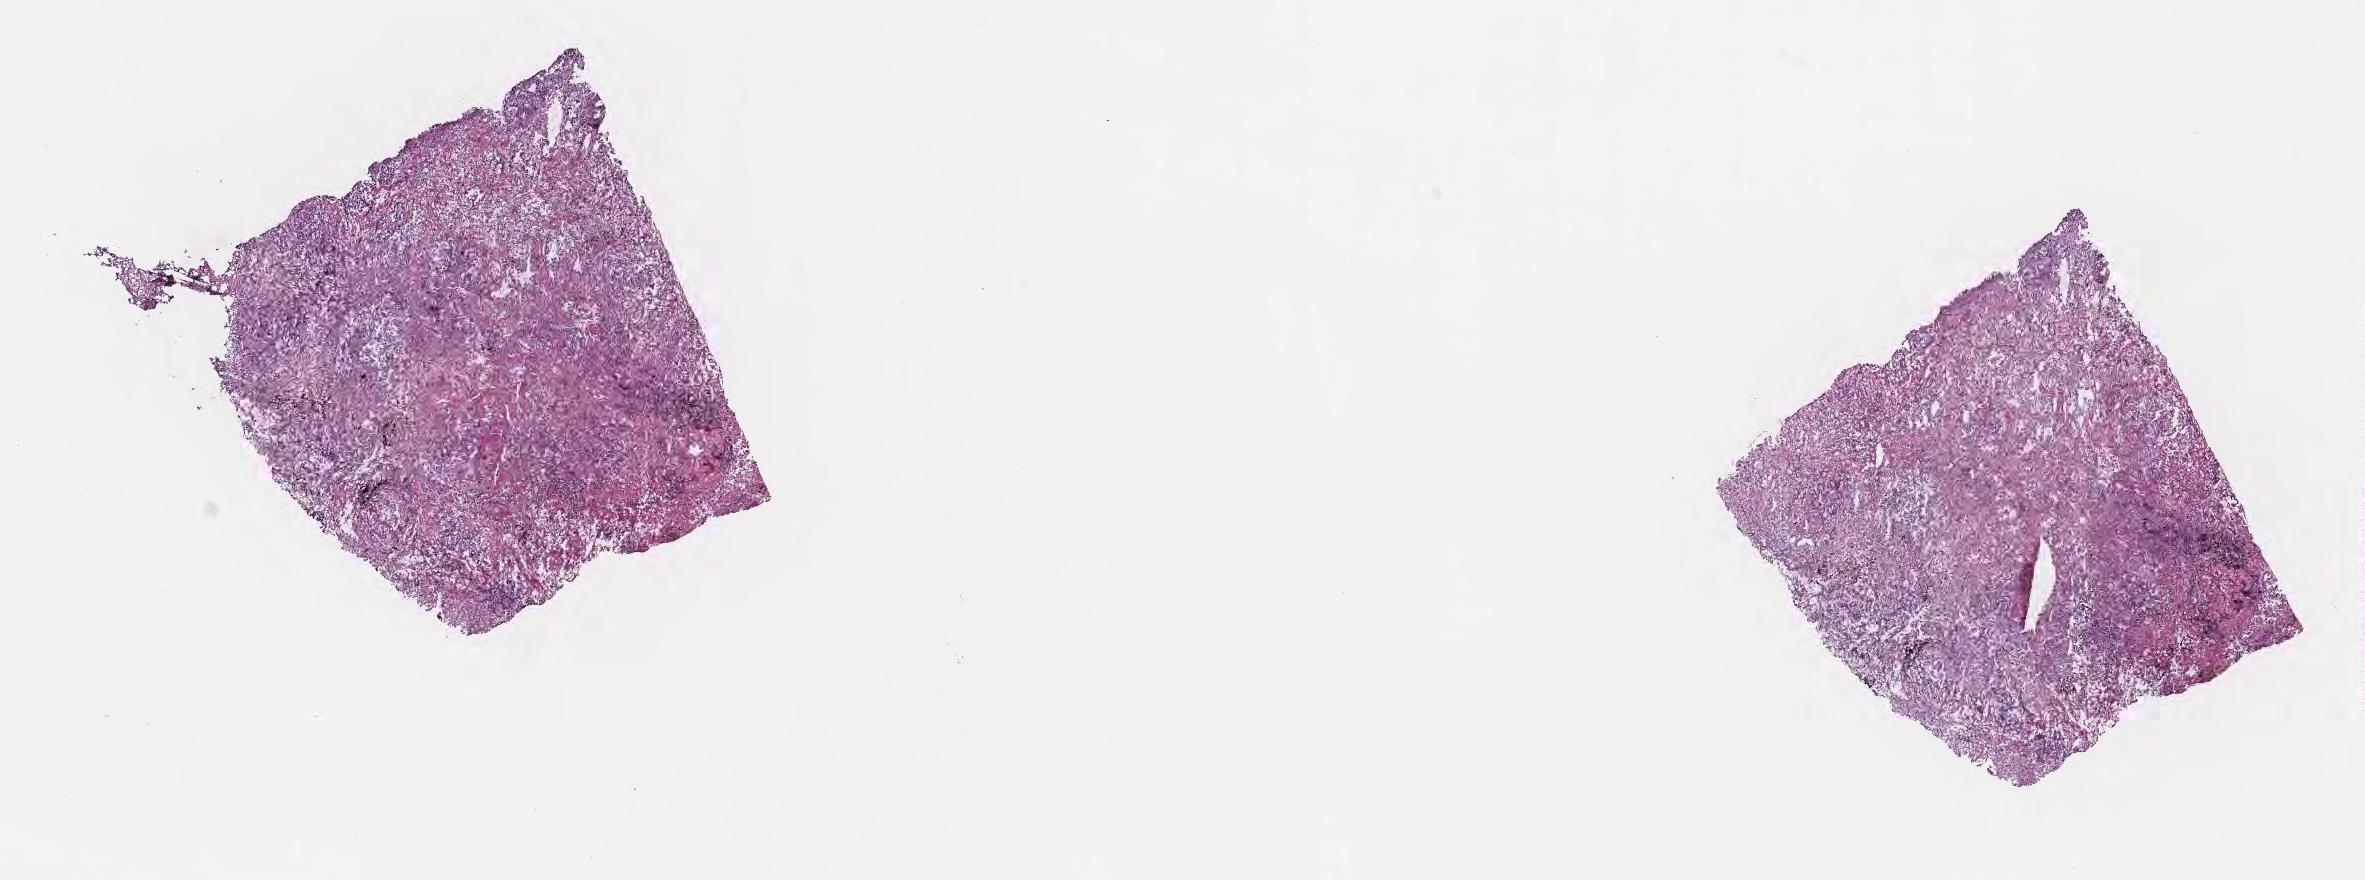
H&E whole-slide image, low-resolution overview of the scanned area, about 19.1 x 7.1 mm; cryosection; primary tumor; site: upper lobe of left lung. Patient male; 53 years old. Pathologist review of this section (percent, as recorded): tumor cells 70%, tumor nuclei 70%, stromal cells 26%, necrosis 2%, normal cells 2%. Infiltration values recorded for this section: lymphocyte infiltration 5%, monocyte infiltration 7%, neutrophil infiltration 5%.
• AJCC pathologic stage: Stage IIIB
• section: top of the tissue portion
• histologic diagnosis: Adenocarcinoma, NOS